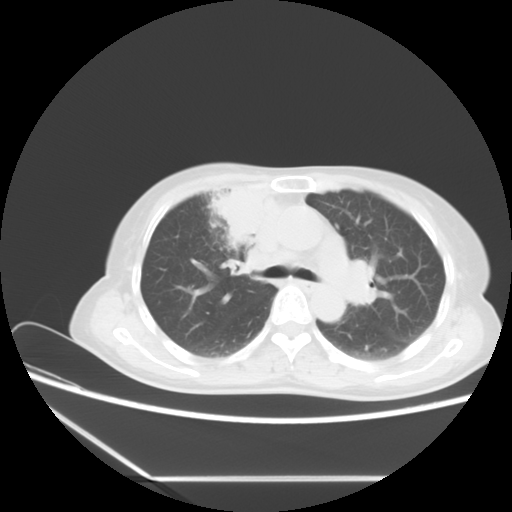
Chest CT, one axial slice. Position 1 of 5 along the scan axis. 120 kVp. Lung window (W 1500 / L -600 HU). 5 mm slice thickness. 512 × 512 image matrix, field of view 350 × 350 mm. Female patient, age 63 years. Case-level facts recorded for this patient, not image findings: clinical TNM (as recorded): T2b N1 M0.
Structures marked on this image (rectangle marked by the reading radiologist):
- lung tumour (recorded histology: adenocarcinoma): box from (x=207, y=175) to (x=276, y=258) px